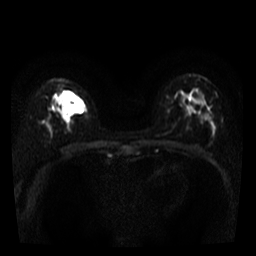
Breast MRI, one axial slice. Slice 22 of 40 in the series (ordered by position). Diffusion-weighted series; image 2 of 4 stored at this slice position (different b-values; order by instance number). 3 T. 256 × 256 image matrix, field of view 280 × 280 mm. Female patient.
Structures marked on this image (manually delineated by an expert):
- tumour on diffusion-weighted imaging: bounding box (x1, y1, x2, y2) in pixels: (62, 91, 84, 114)